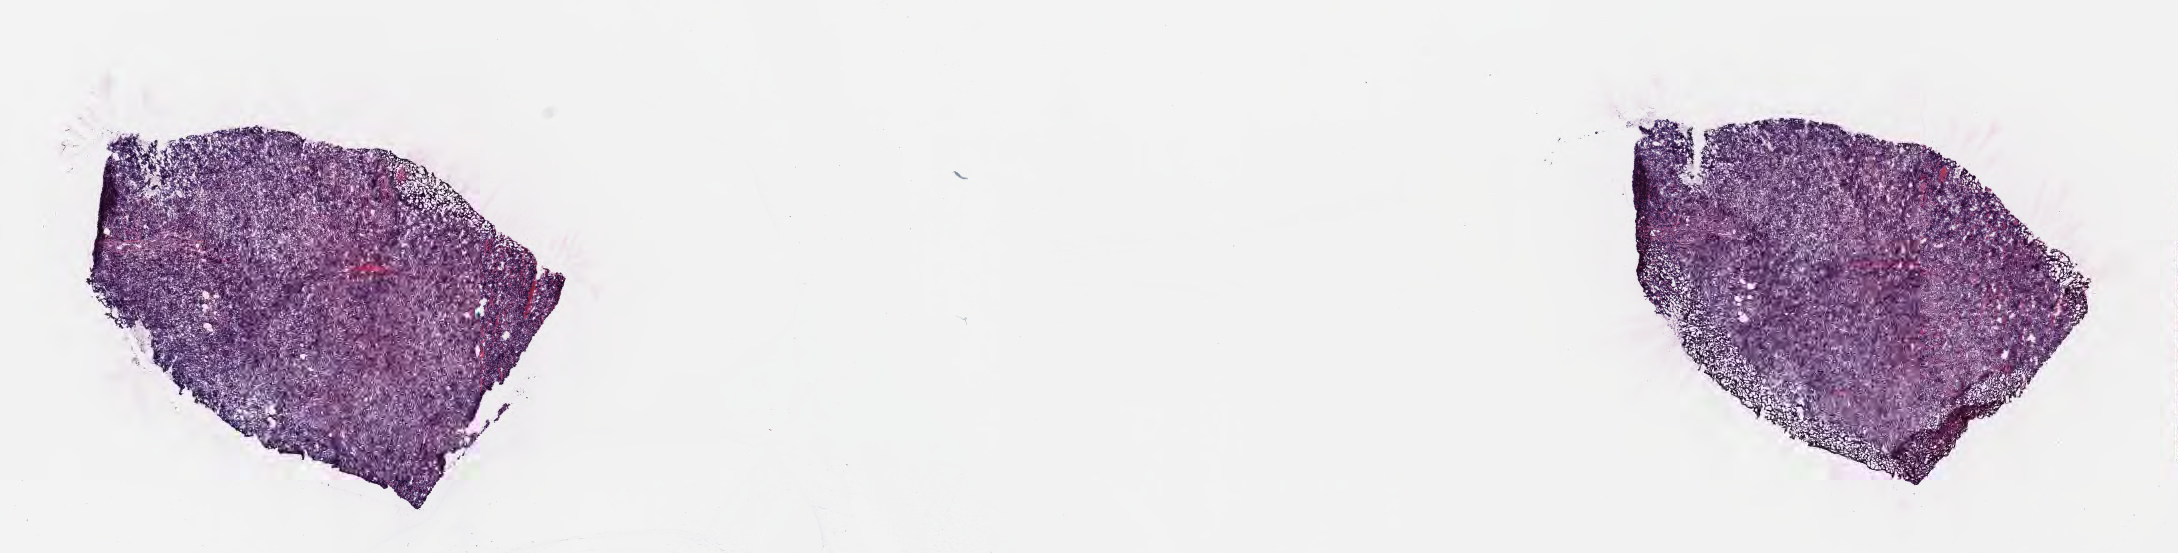
Digitized H&E-stained section — a low-resolution overview of the entire scanned area, about 17.6 x 4.5 mm, frozen section, specimen: primary tumor, site: buccal mucosa. Male patient; age at initial diagnosis 7 years. Composition of this section per pathologist review: tumor cells 95%, tumor nuclei 90%, stromal cells 3%, necrosis 2%, normal cells 0%. Infiltration values recorded for this section: lymphocyte infiltration 60%, monocyte infiltration 25%, neutrophil infiltration 0%.
Diagnosis: Burkitt lymphoma, NOS. Section: bottom of the tissue portion. Ann Arbor stage (patient): Stage I.